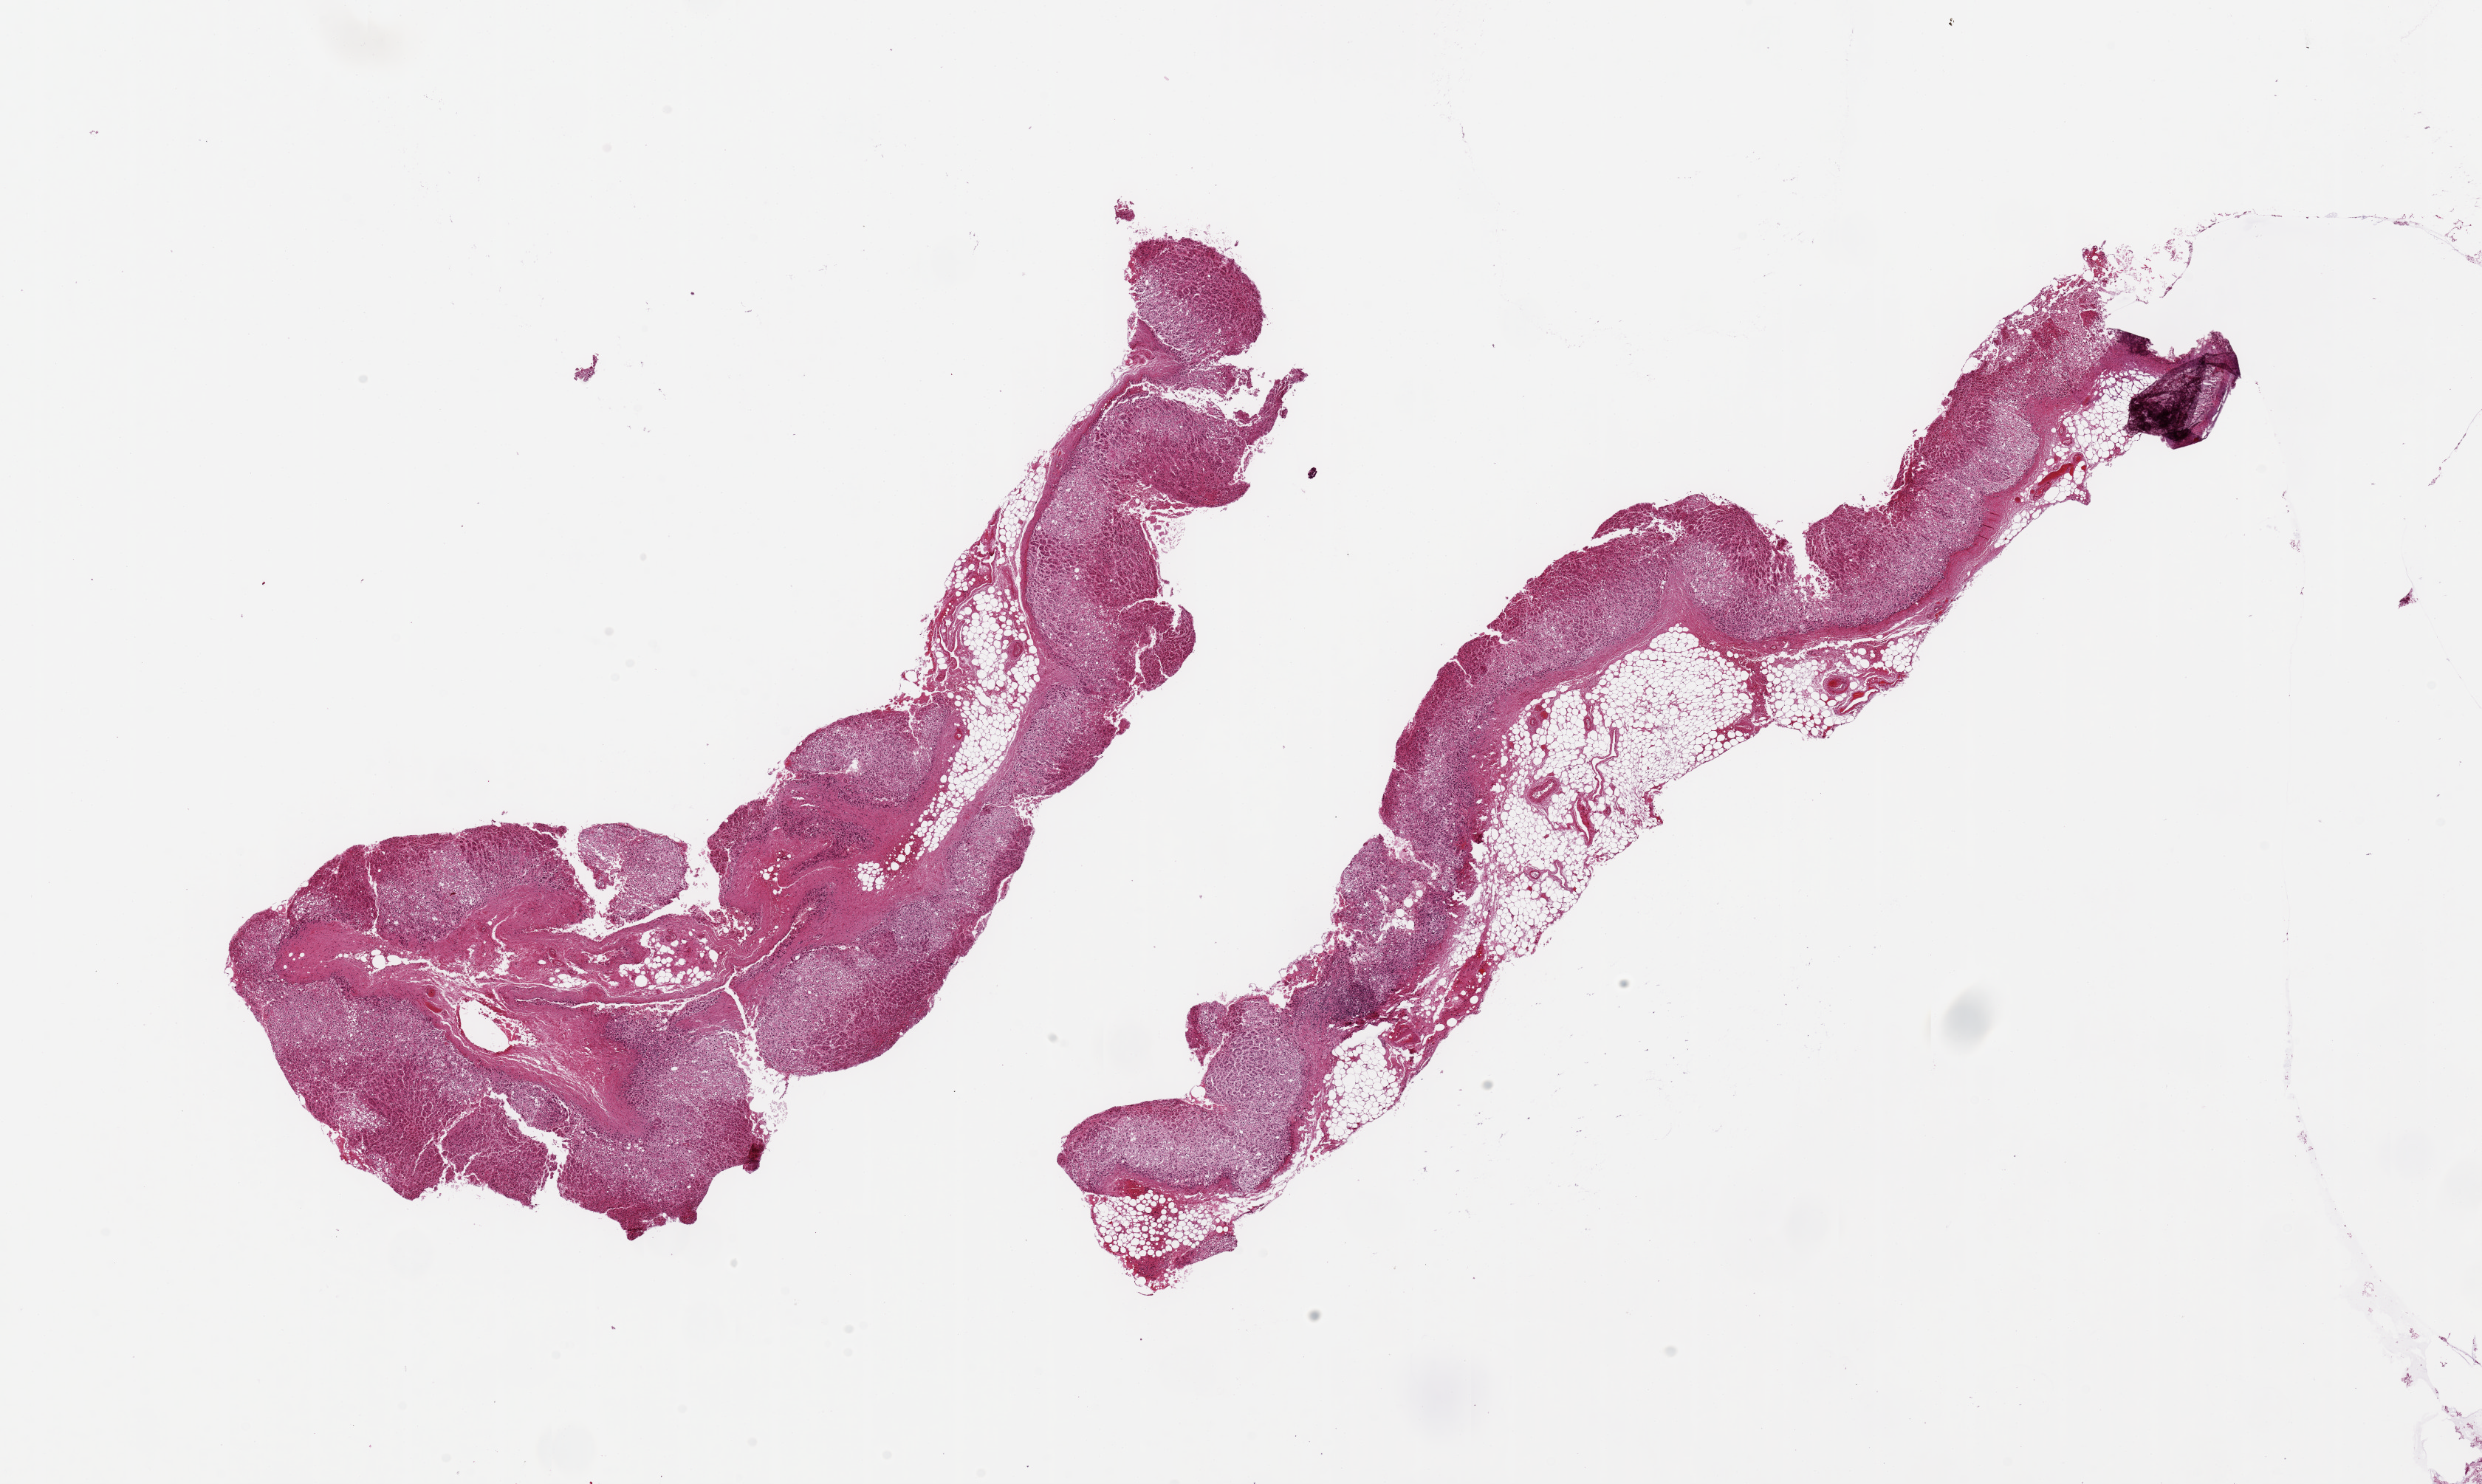
Digitized H&E-stained section, brightfield — shown as a low-resolution overview of the whole scanned area (about 26.6 x 15.9 mm). PAXgene-fixed, paraffin-embedded tissue. Section of adrenal gland (target tissue). Tissue donor sample.
Review note (as recorded): 2 pieces ~14x3mm; Fat is 10-40% of specimens.